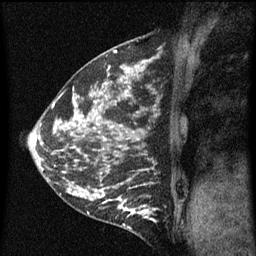
Breast MRI (dynamic contrast-enhanced), one sagittal slice. Slice 20 of 60 in the series (ordered by position). Dynamic contrast-enhanced series, image 2 of 5 at this slice position (ordered by acquisition). 1.5 T. TE 4.2 ms, TR 8 ms. 256 × 256 image matrix. Female patient, age 35 years.
Outlined on this slice (semi-automatic segmentation, software-assisted and operator-edited):
- analysis volume of interest (the breast-tissue region the enhancement analysis was run in; not a lesion): bounding box (x1, y1, x2, y2) in pixels: (118, 196, 157, 229)
- tumour enhancement mask (voxels above the 70 % enhancement threshold inside the analysis volume of interest): (119, 196, 157, 223)